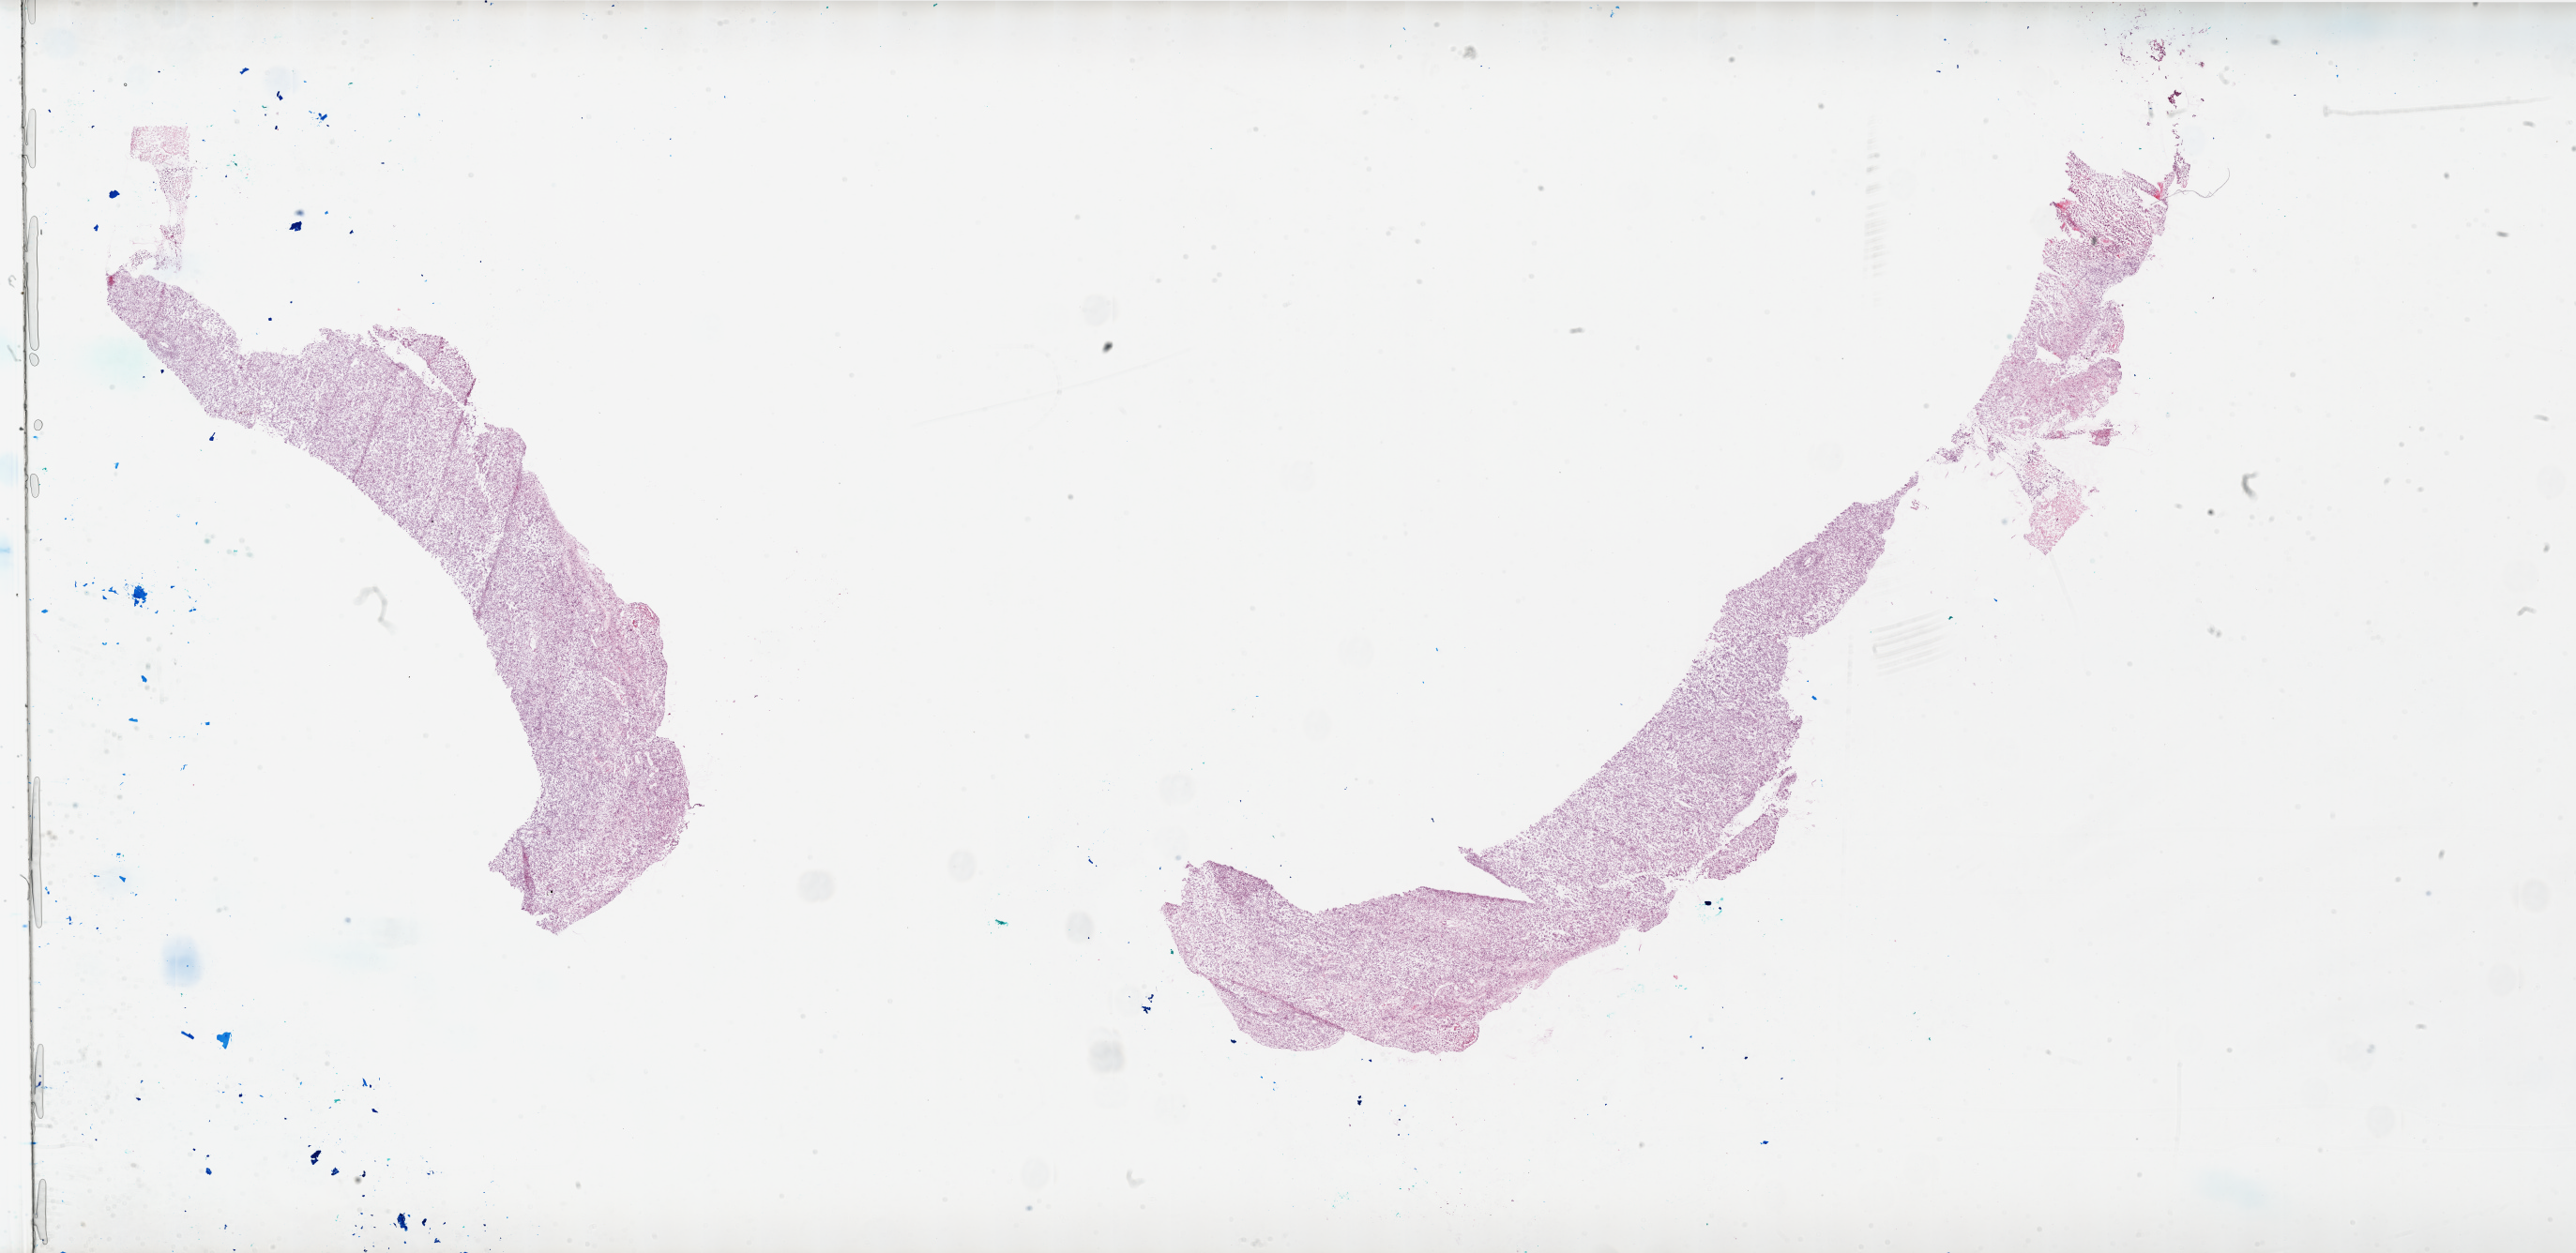
H&E whole-slide image — a low-resolution overview of the entire scanned area, about 44.0 x 21.4 mm (slide scanned at 20x), frozen section, primary tumour sample from the brain. Female, age 20 years at initial diagnosis. Composition of this section per pathologist review: tumour cells 90%, tumour nuclei 100%, normal cells 0%, stromal cells 0%, necrosis 10%. Inflammatory infiltration, as recorded: lymphocyte infiltration 10%, monocyte infiltration 0%, neutrophil infiltration 0%.
Diagnosis: Glioblastoma.